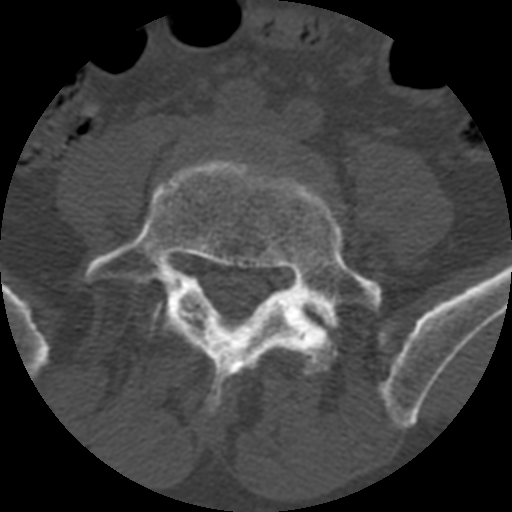
CT including the spine, one axial slice. Position 258 of 399 along the scan axis. Reconstruction kernel STANDARD. 120 kVp. Bone window (W 1800 / L 400 HU). 1.25 mm slice thickness. 512 × 512 image matrix, field of view 160 × 160 mm. Patient age 71 years. From the clinical record (not read from this slice): primary cancer: prostate.
Outlined on this slice (semi-automatically segmented with operator editing):
- L5 vertebra: bounding box [x1, y1, x2, y2] px = [83, 159, 383, 418]